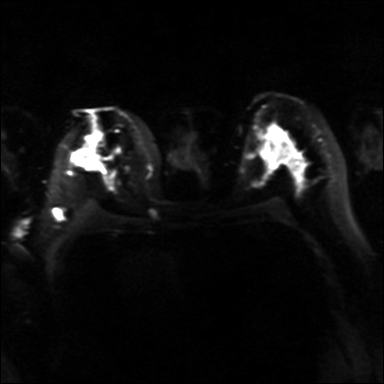
Breast MRI, one axial slice; slice 20 of 36 in the series (ordered by position); diffusion-weighted series; image 2 of 4 stored at this slice position (different b-values; order by instance number); 3 T; 4 mm slice thickness; 384 × 384 image matrix, field of view 320 × 320 mm. Female patient.
Structures marked on this image (expert manual segmentation):
- tumour on diffusion-weighted imaging: bounding box (x1, y1, x2, y2) in pixels: (73, 150, 99, 167)